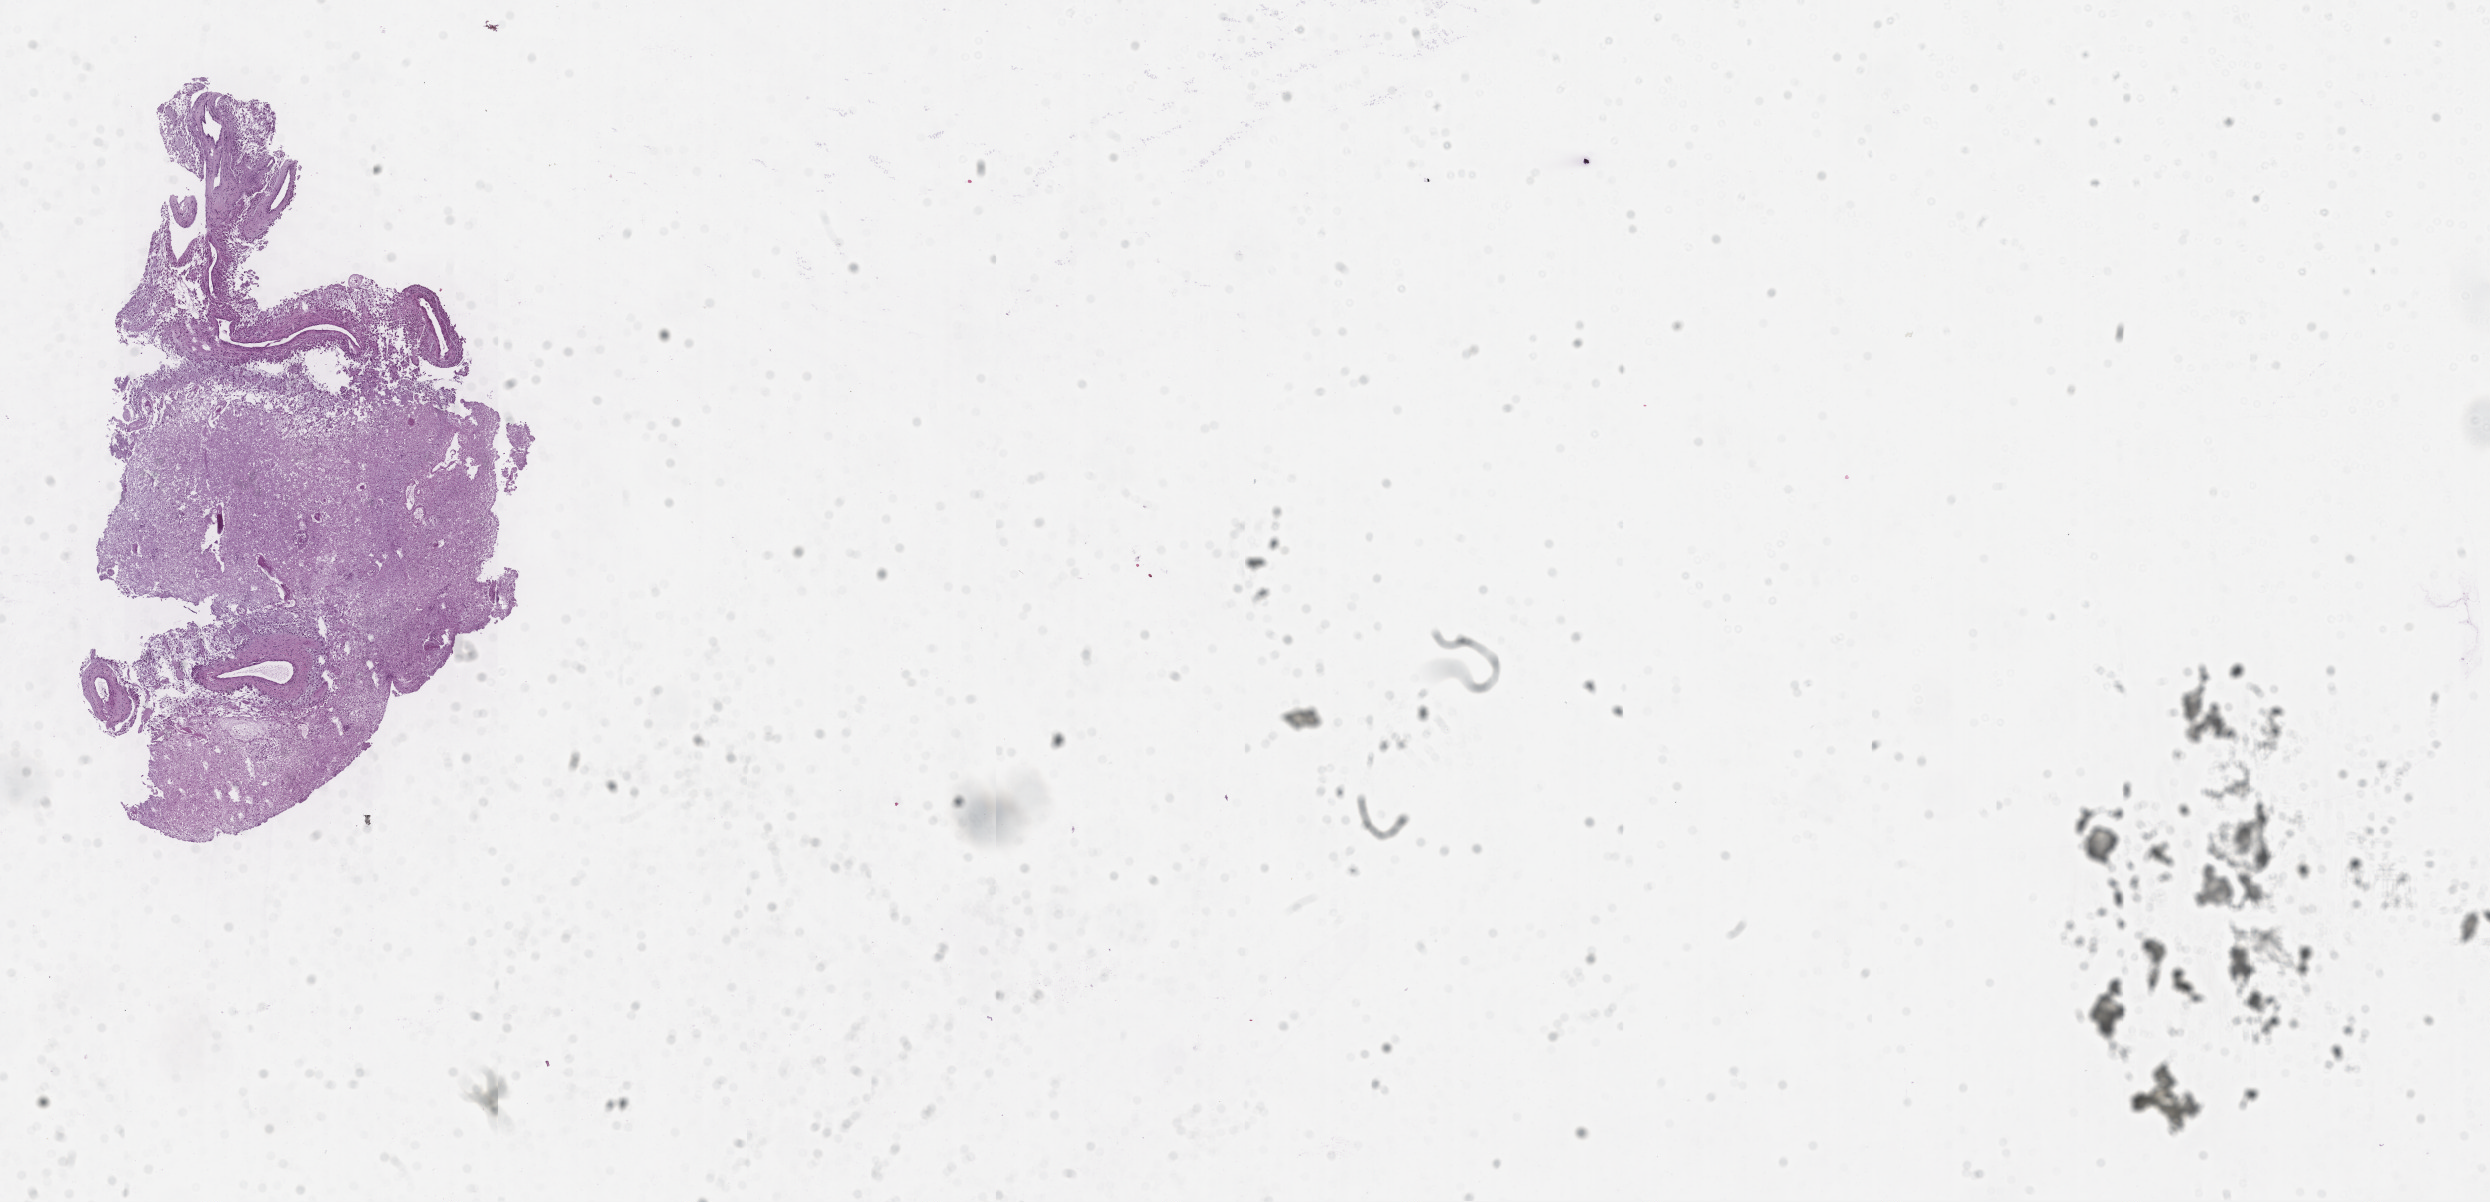
Whole-slide histology image, H&E — low-resolution overview of the scanned area, about 20.1 x 9.7 mm. Tumour tissue sample, brain. Male, 78 y/o.
Diagnosis: Glioblastoma.